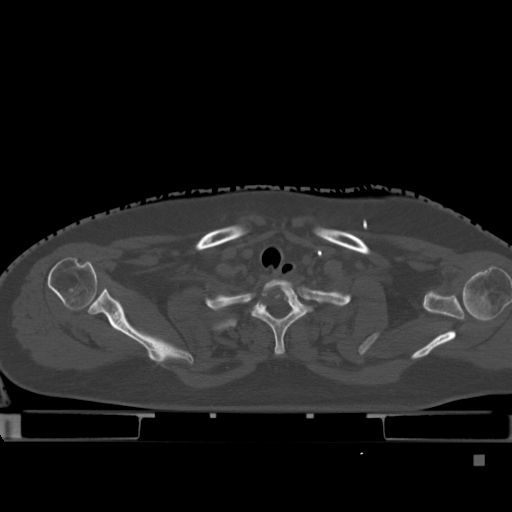
CT including the spine, one axial slice; slice 370 of 495 in the series (ordered by position); bone window (W 1800 / L 400 HU); 512 × 512 image matrix. Female patient, age 33 years. From the clinical record (not read from this slice): primary cancer: breast; vertebrae with lytic lesions (as recorded): T1.
Outlined on this slice (semi-automatic segmentation, software-assisted and operator-edited):
- T1 vertebra: bounding box (x1, y1, x2, y2) in pixels: (253, 282, 306, 355)
- T2 vertebra: (242, 324, 245, 326)